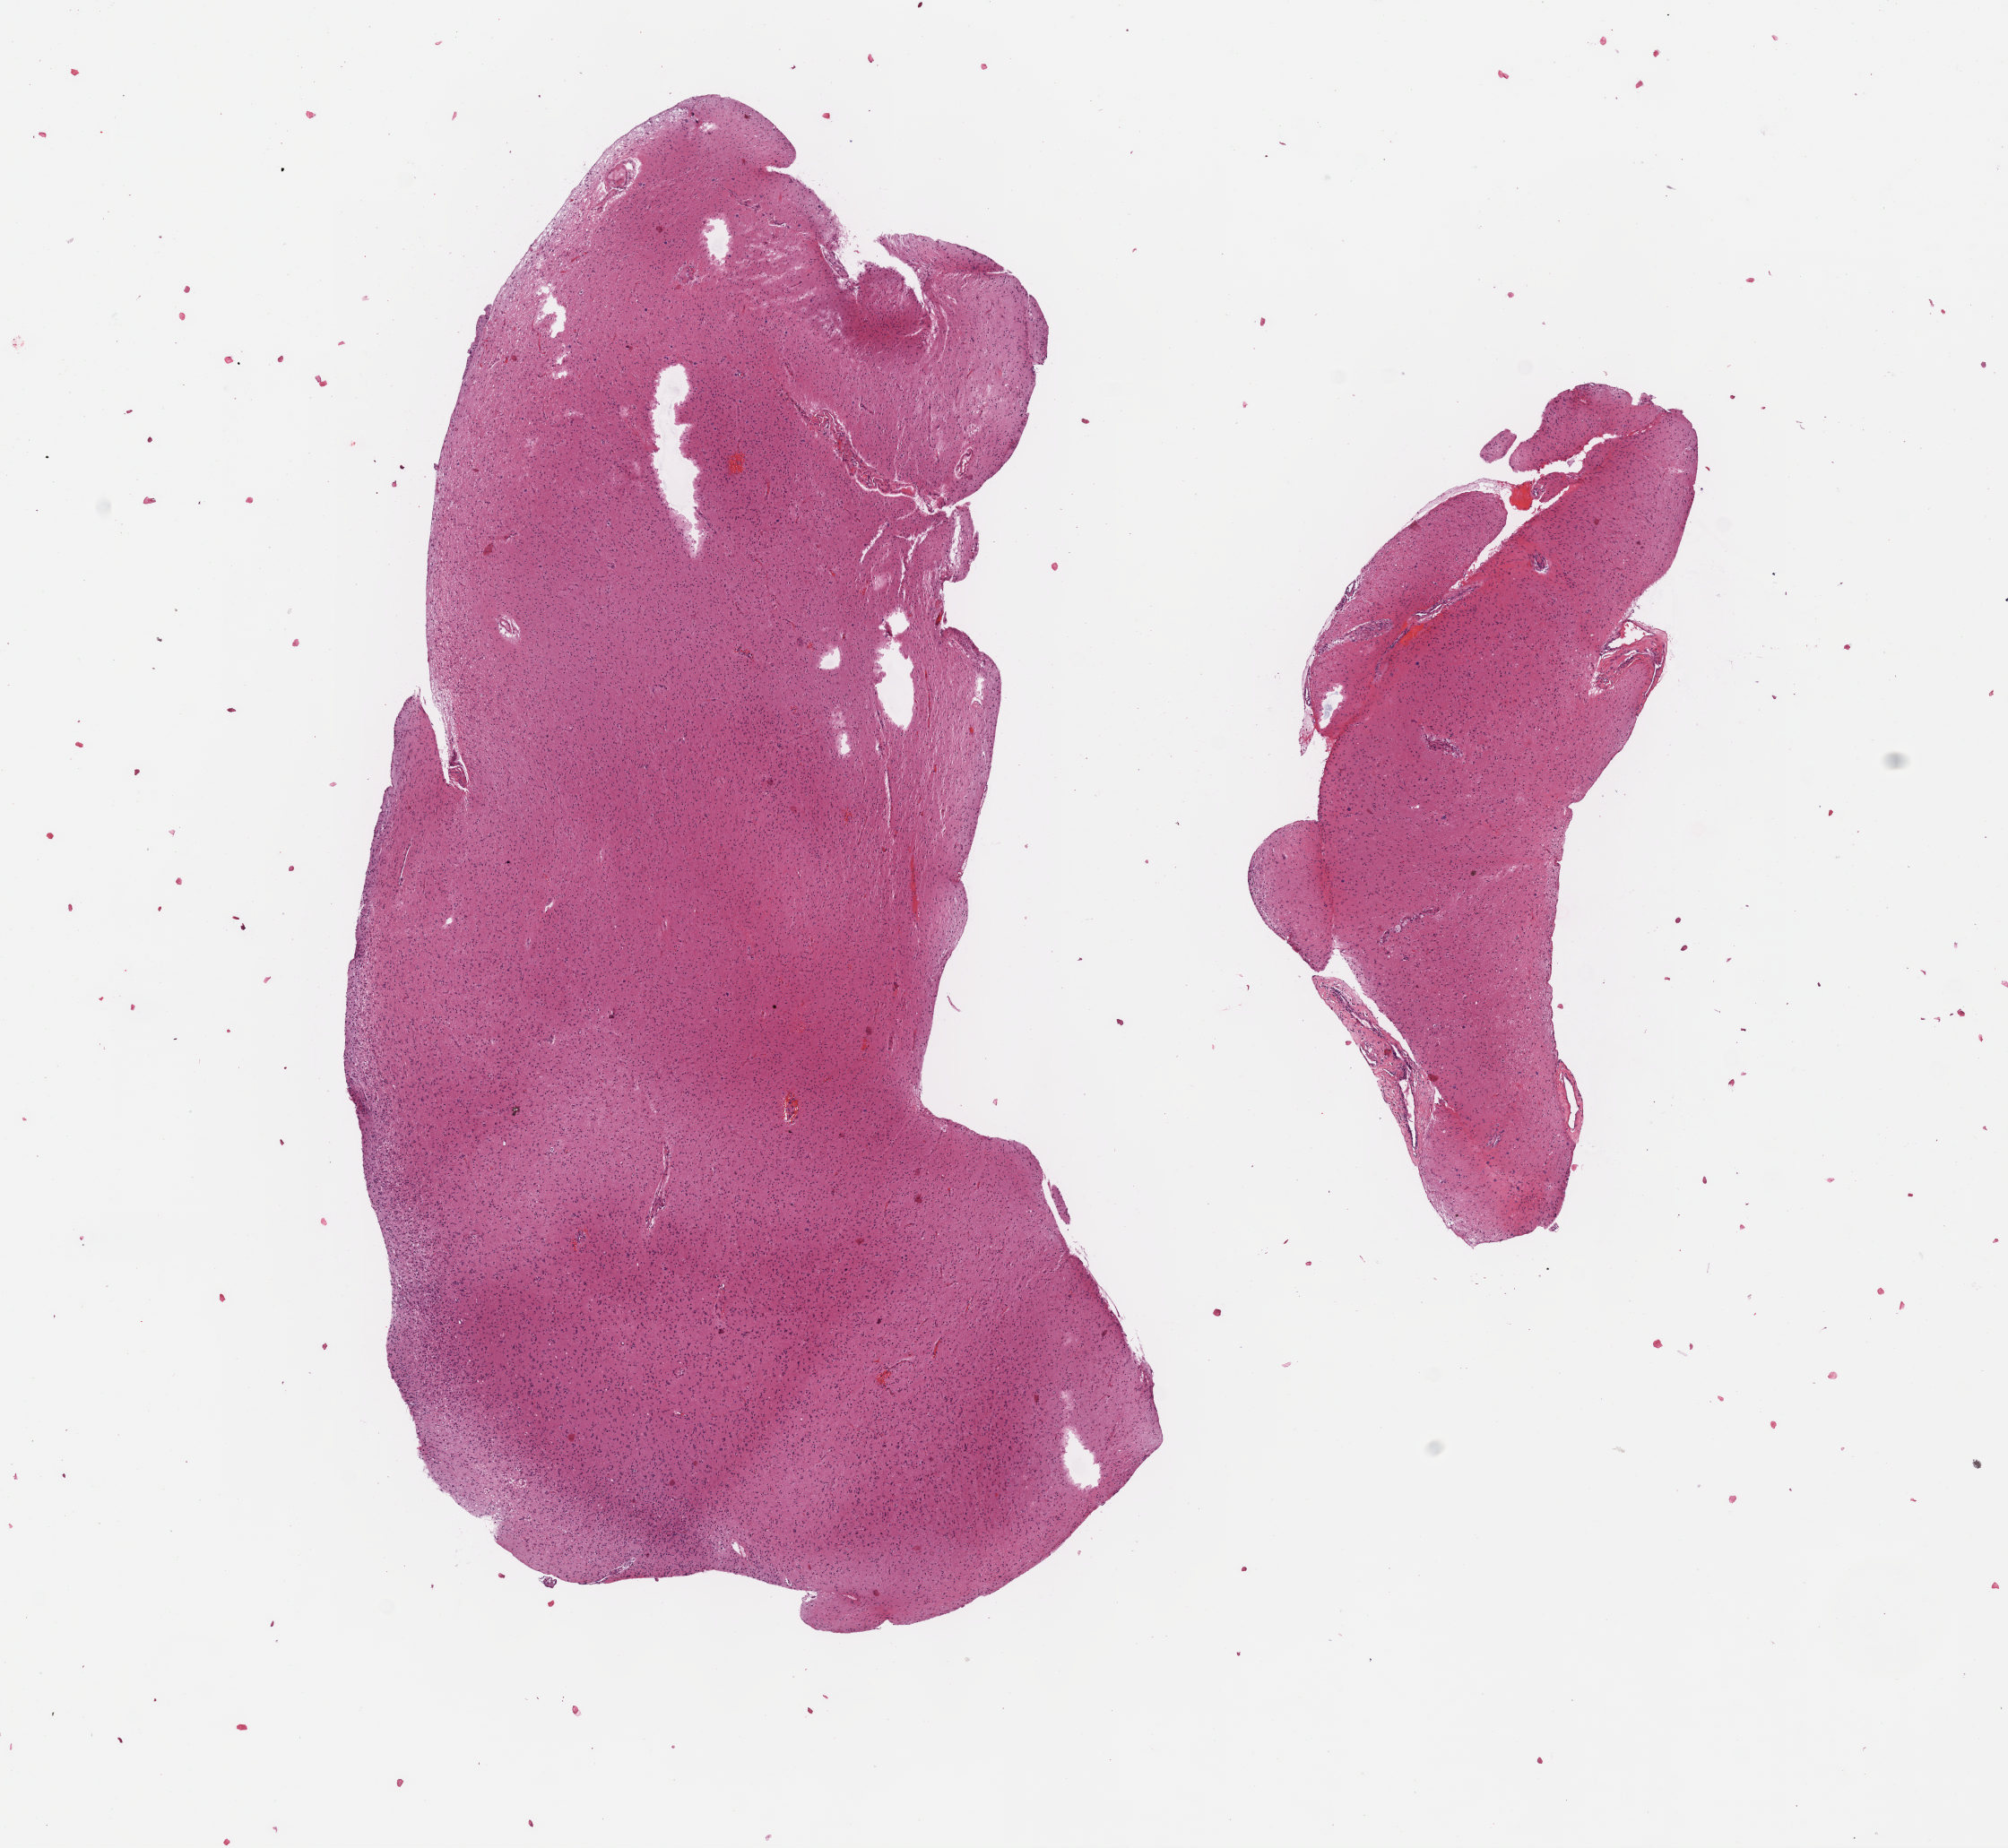
H&E-stained whole-slide image, low-resolution overview of the scanned area, about 9.1 x 8.3 mm, formalin-fixed paraffin-embedded (FFPE) diagnostic section, primary tumour sample from the brain. Male, age 53 years at initial diagnosis. Histologic grade: G3 (poorly differentiated).
Diagnosis: Oligodendroglioma, anaplastic. Laterality: left.